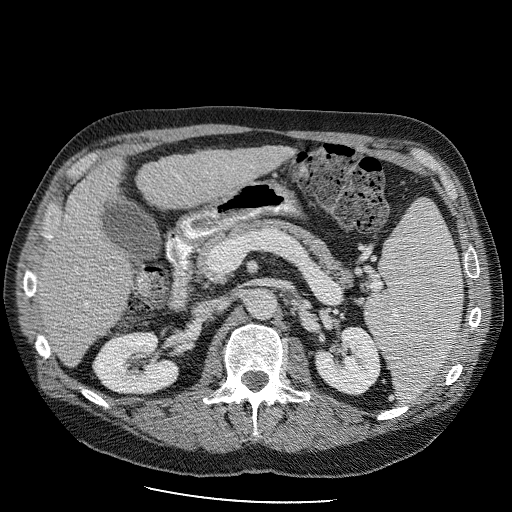
Contrast-enhanced abdominal CT (liver protocol), one axial slice; reconstruction kernel STANDARD; 120 kVp; soft-tissue window (W 400 / L 40 HU); 512 × 512 image matrix, field of view 400 × 400 mm. Case-level facts recorded for this patient, not image findings: diagnosis: hepatocellular carcinoma (patient treated with transarterial chemoembolisation; whether this scan precedes or follows treatment is not stated here); TNM stage (as recorded): Stage-II; Child-Pugh class: B; tumour differentiation: moderately differentiated; tumour nodularity: uninodular.
Annotated regions visible in this slice (semi-automatically segmented with operator editing):
- liver parenchyma outside the tumour (the mass and vessels are separate outlines, so this box may not span the whole liver): box from (x=36, y=144) to (x=297, y=364) px